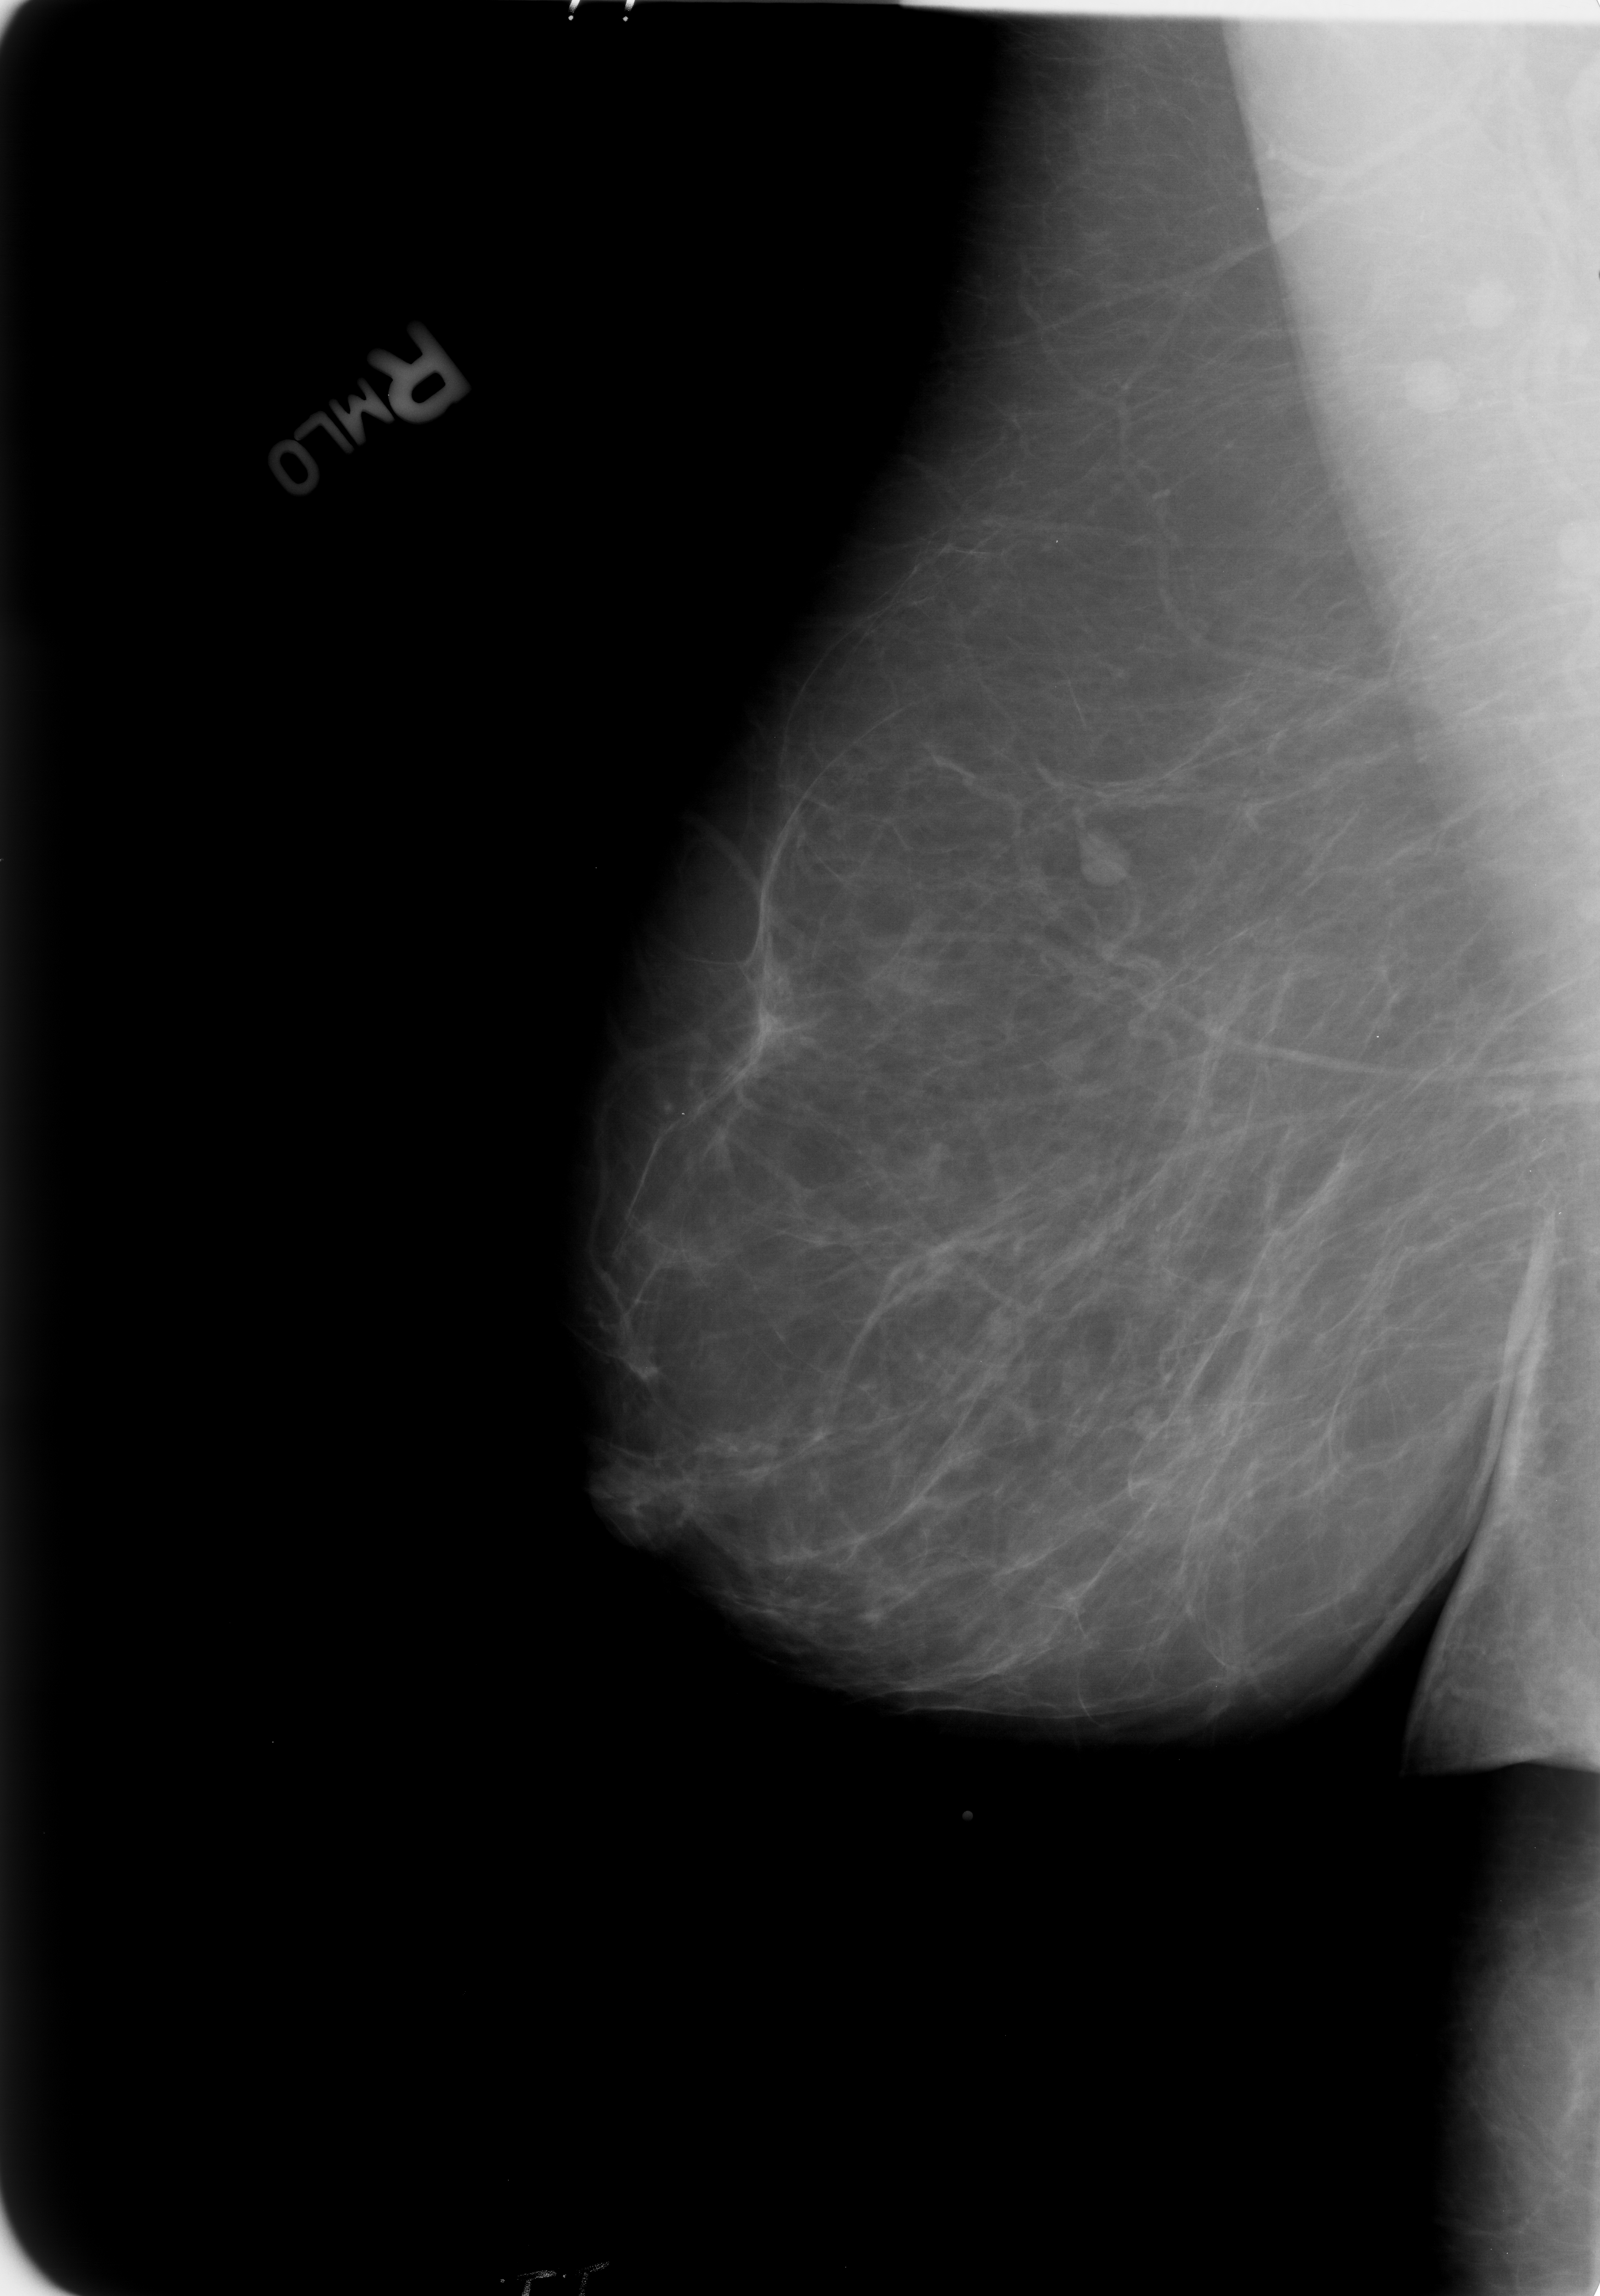
Digitized screen-film mammogram; right breast; MLO view; breast composition: almost entirely fatty (BI-RADS density category 1 of 4).
Finding: mass, shape lymph node; BI-RADS assessment category 2; subtlety rating 3 on a 1 (subtle) to 5 (obvious) scale; benign without callback (not worked up further).